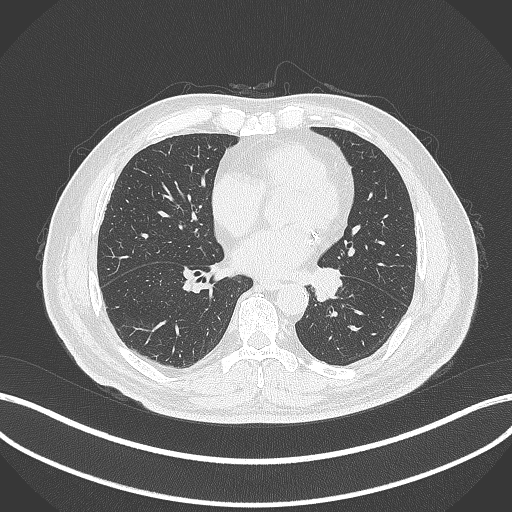
Chest CT, one axial slice; reconstruction kernel B70f; lung window (W 1500 / L -600 HU); 1 mm slice thickness; 512 × 512 image matrix, field of view 400 × 400 mm. Patient: male, 71 years. Case-level facts recorded for this patient, not image findings: clinical TNM (as recorded): T1b N0 M0.
Annotated regions visible in this slice (bounding box drawn by a radiologist):
- lung tumour (recorded histology: squamous cell carcinoma): bounding box [x1, y1, x2, y2] px = [309, 263, 347, 304]